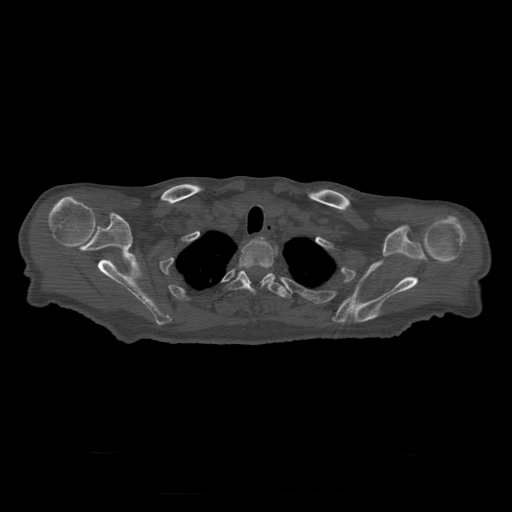
CT including the spine, one axial slice; position 266 of 397 along the scan axis; 120 kVp; bone window (W 1800 / L 400 HU); 1.25 mm slice thickness; 512 × 512 image matrix, field of view 510 × 510 mm. Patient age 73 years. From the clinical record (not read from this slice): primary cancer: prostate.
Structures marked on this image (semi-automatic segmentation, software-assisted and operator-edited):
- T2 vertebra: bounding box [x1, y1, x2, y2] px = [239, 239, 276, 282]
- T3 vertebra: [225, 271, 291, 298]